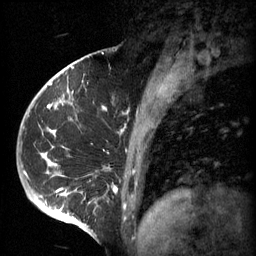
Breast MRI (dynamic contrast-enhanced), one sagittal slice; 3 images stored at this slice position (order not interpretable as contrast timing); 1.5 T; TE 4.2 ms, TR 11 ms; 2 mm slice thickness; 256 × 256 image matrix, field of view 200 × 200 mm. Female patient, age 51 years.
Outlined on this slice (semi-automatic segmentation, software-assisted and operator-edited):
- analysis volume of interest (the breast-tissue region the enhancement analysis was run in; not a lesion): bounding box [x1, y1, x2, y2] px = [48, 82, 161, 197]
- tumour enhancement mask (voxels above the 70 % enhancement threshold inside the analysis volume of interest): [48, 82, 161, 195]